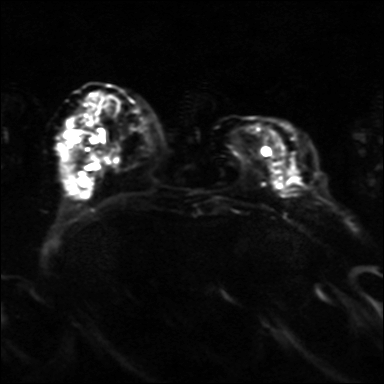
Breast MRI, one axial slice. Position 11 of 36 along the scan axis. Diffusion-weighted series; image 2 of 4 stored at this slice position (different b-values; order by instance number). 3 T. 4 mm slice thickness. 384 × 384 image matrix, field of view 320 × 320 mm. Female patient.
Annotated regions visible in this slice (outlined manually by an expert reader):
- tumour on diffusion-weighted imaging: bounding box [x1, y1, x2, y2] px = [272, 136, 299, 178]